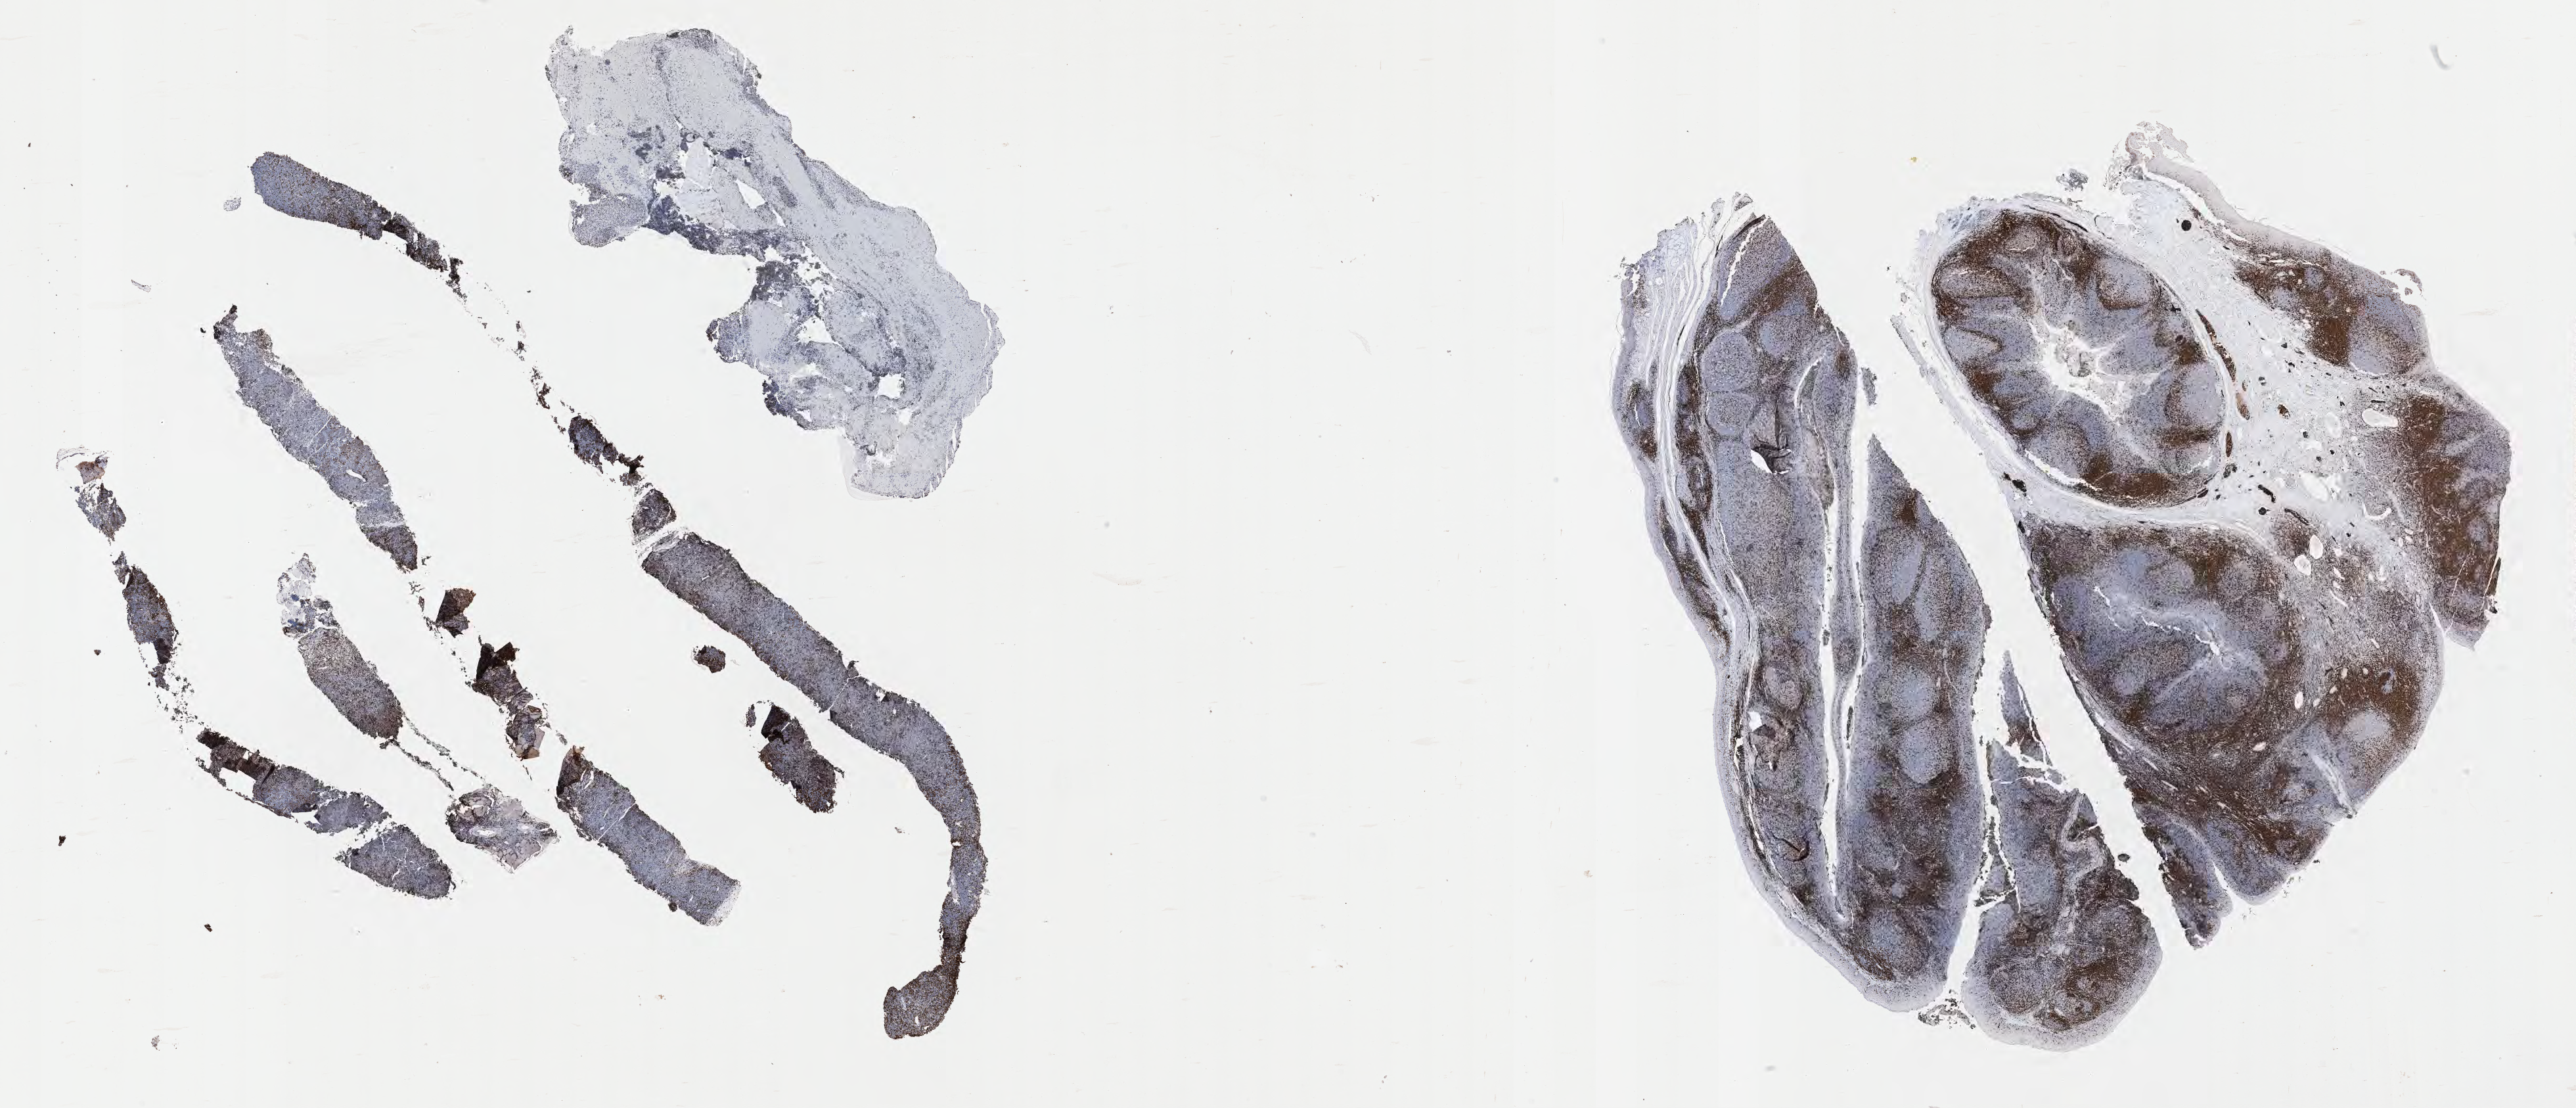
IHC for CD3, whole-slide image — whole scanned area (about 31.7 x 13.6 mm) shown as a low-resolution overview. Specimen: tumor tissue. Patient male; aged 29.
Diagnosis: Burkitt lymphoma, NOS.